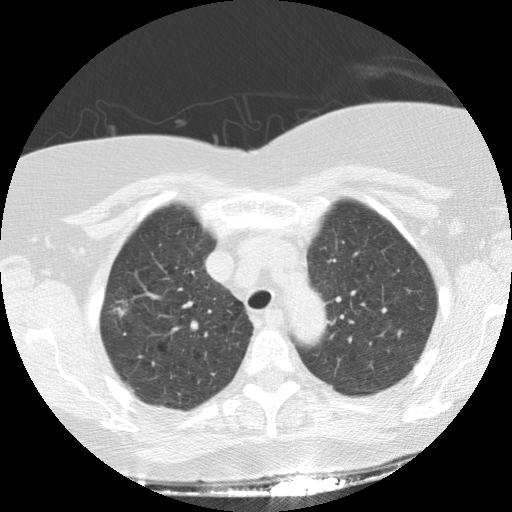
Low-dose screening chest CT, one axial slice. Slice 108 of 136 in the series (ordered by position). 120 kVp. Lung window (W 1500 / L -600 HU). 2.5 mm slice thickness. 512 × 512 image matrix, field of view 330 × 330 mm.
Structures marked on this image (expert manual segmentation):
- lesion 1 (tumor, upper lobe of right lung): box from (x=113, y=307) to (x=127, y=317) px